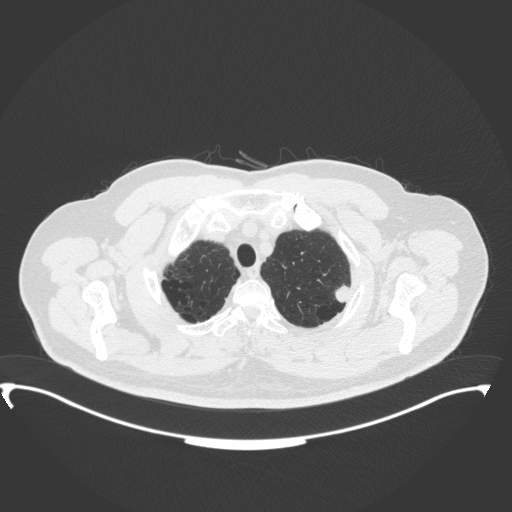
Chest CT, one axial slice. Position 324 of 350 along the scan axis. Reconstruction kernel B31f. Lung window (W 1500 / L -600 HU). 1 mm slice thickness. 512 × 512 image matrix, field of view 459 × 459 mm. Patient: male, 64 years. From the clinical record (not read from this slice): clinical TNM (as recorded): T1c N1 M1.
Annotated regions visible in this slice (rectangle marked by the reading radiologist):
- lung tumour (recorded histology: adenocarcinoma): bounding box (x1, y1, x2, y2) in pixels: (331, 280, 352, 305)